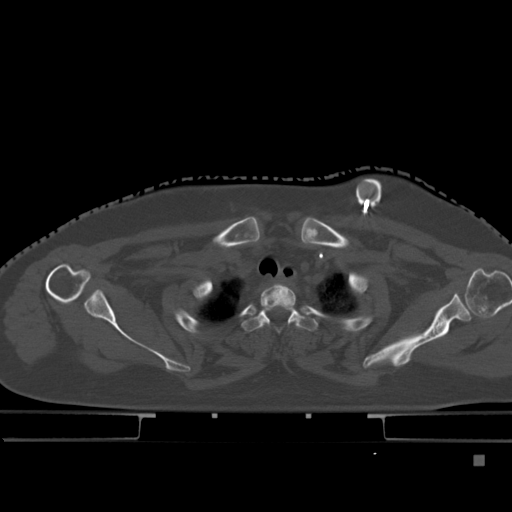
CT including the spine, one axial slice. Position 363 of 495 along the scan axis. Bone window (W 1800 / L 400 HU). 1.5 mm slice thickness. 512 × 512 image matrix. Patient: female, 33 years. From the clinical record (not read from this slice): primary cancer: breast; vertebrae with lytic lesions (as recorded): T1.
Outlined on this slice (semi-automatically segmented with operator editing):
- T1 vertebra: bounding box (x1, y1, x2, y2) in pixels: (260, 284, 296, 327)
- T2 vertebra: (241, 309, 320, 334)